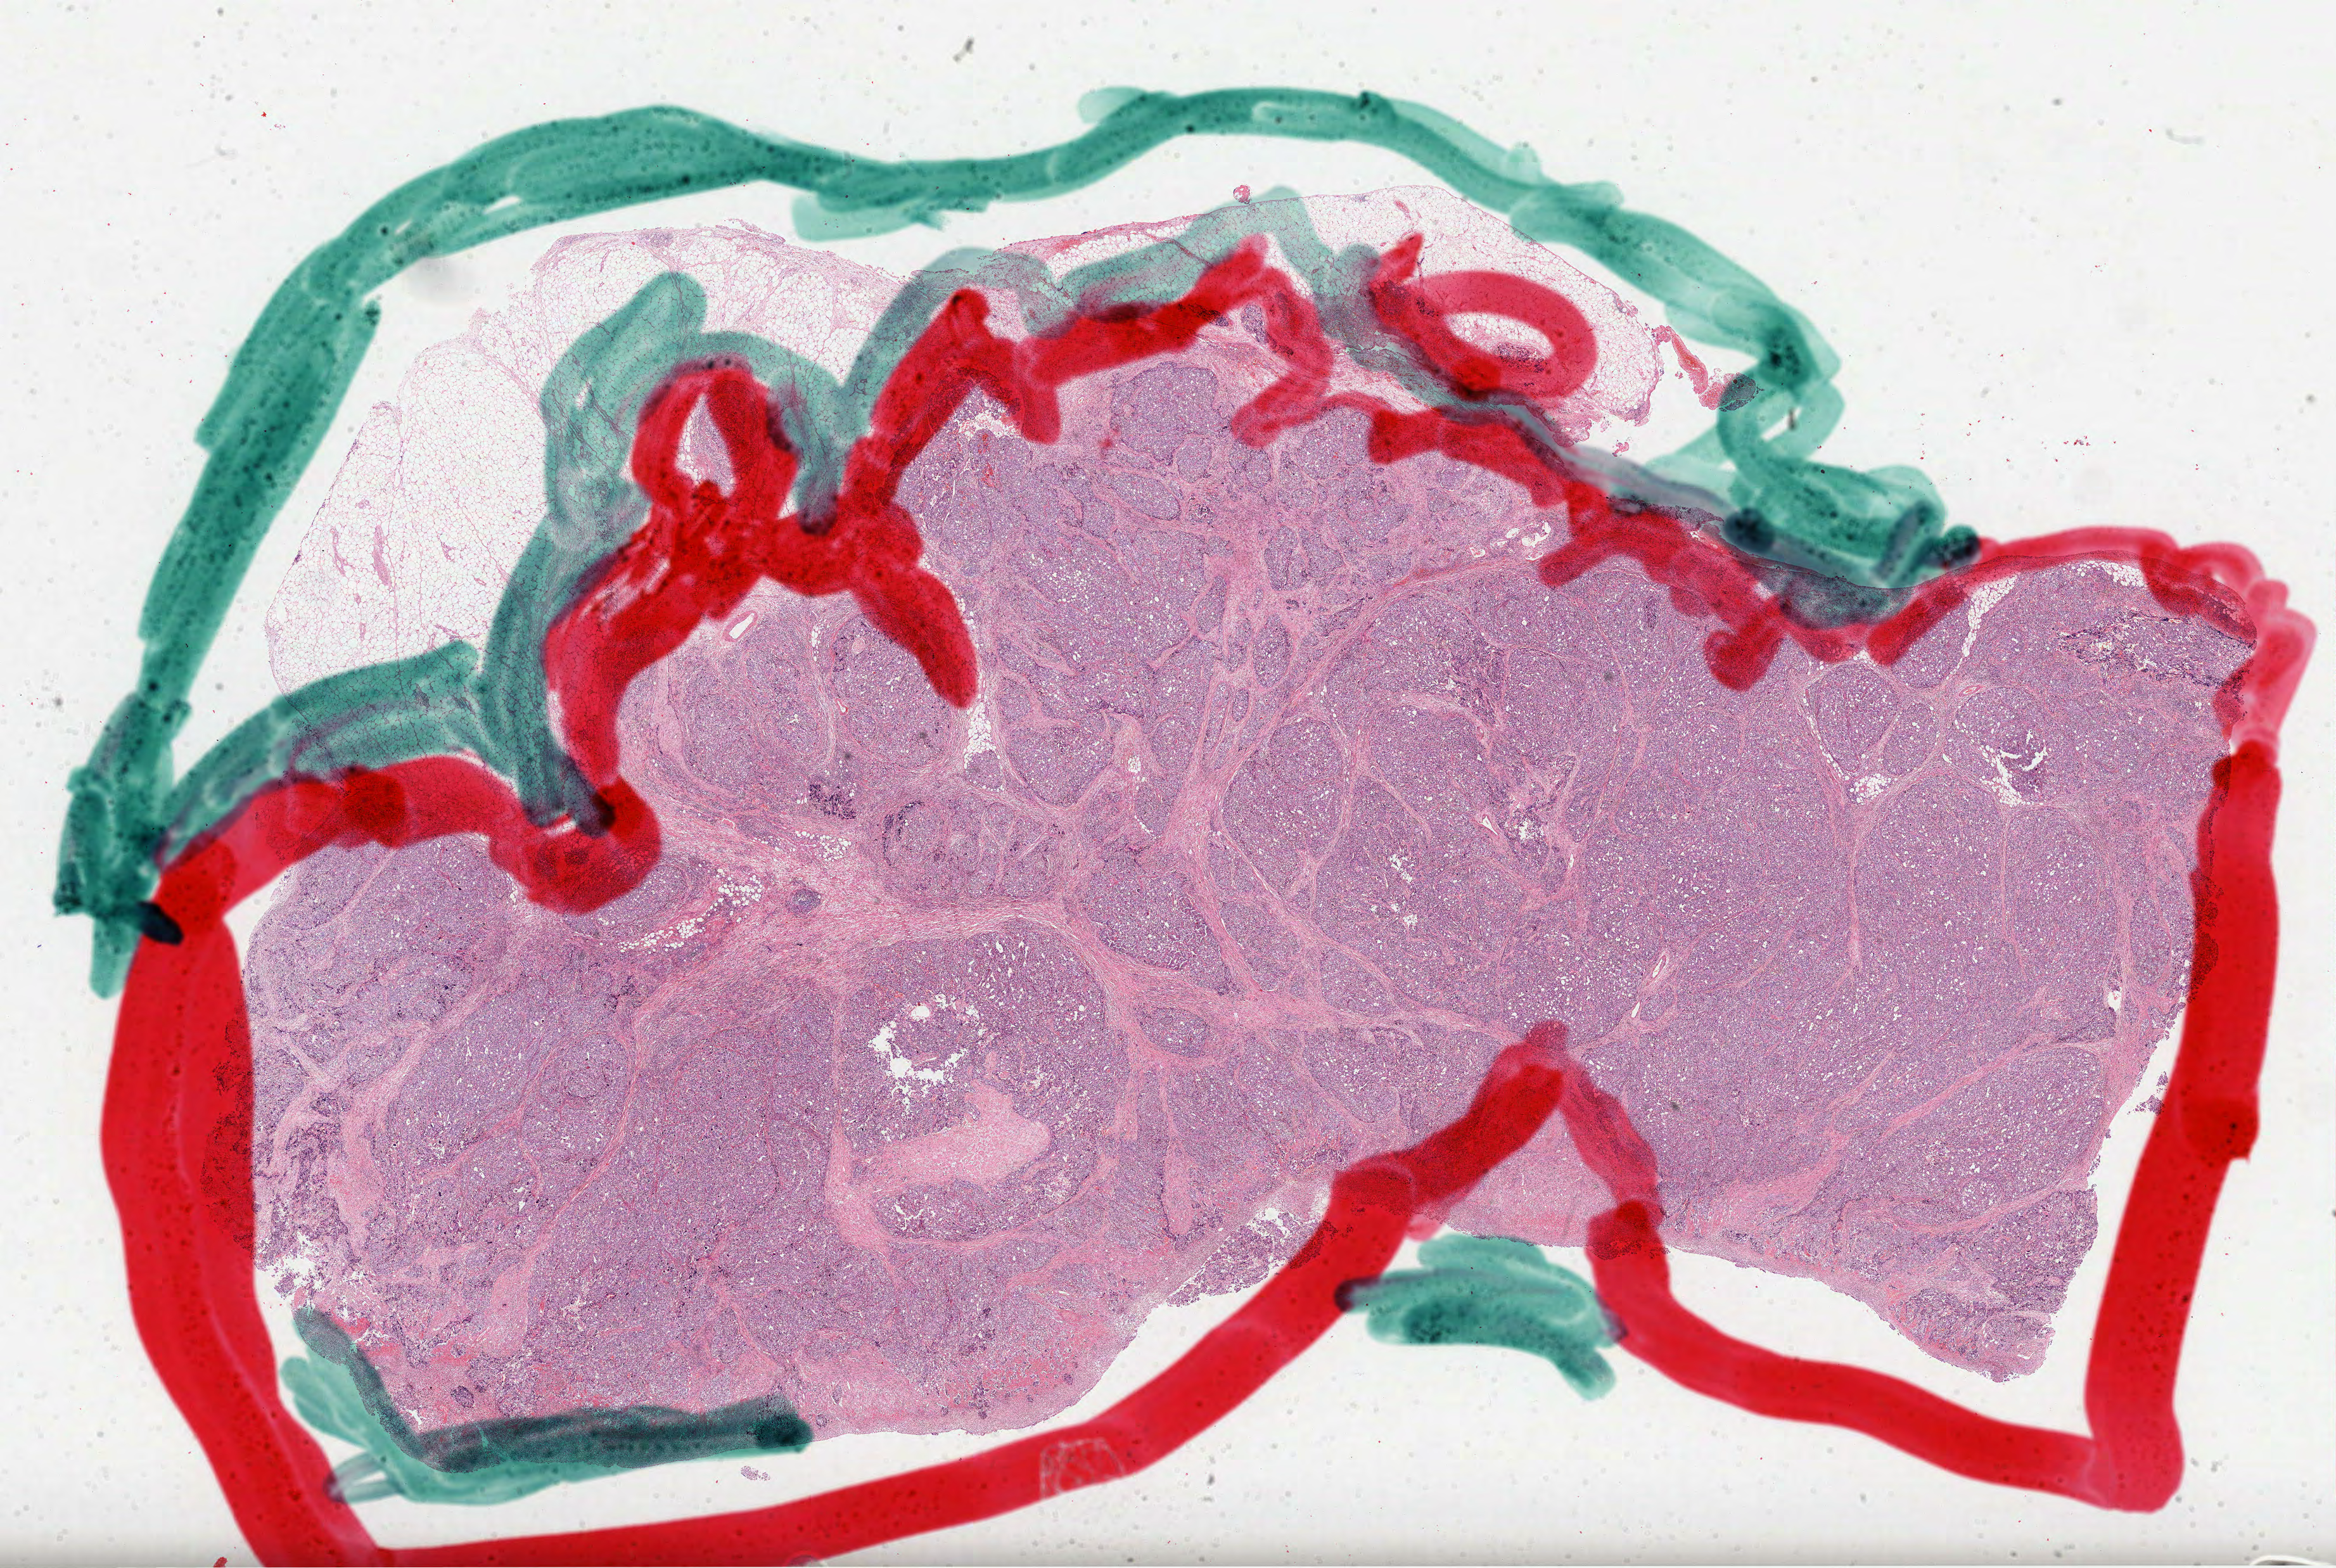
Whole-slide histology image, H&E, low-resolution overview of the scanned area, about 29.7 x 20.0 mm (slide scanned at 40x), formalin-fixed paraffin-embedded (FFPE) diagnostic section, sample: primary tumour, stomach. Patient: male, age at initial diagnosis 59 years.
Histologic diagnosis: Adenocarcinoma, NOS.